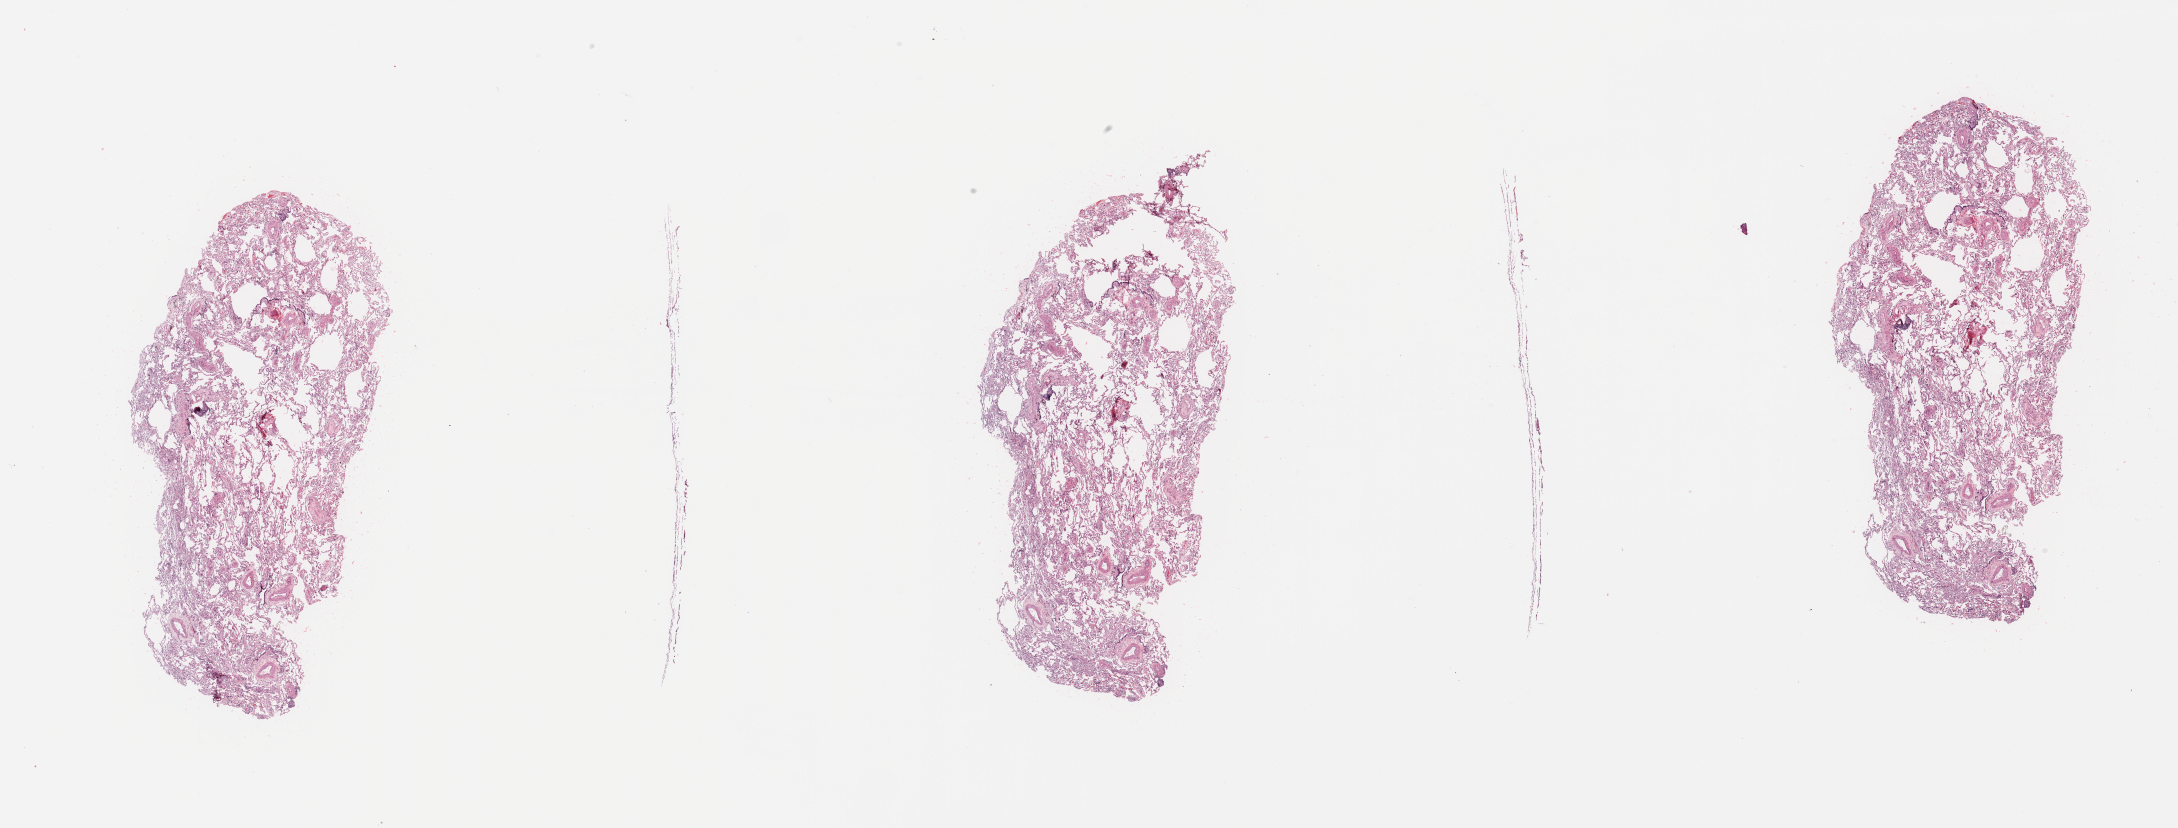
Hematoxylin and eosin (H&E) stained whole-slide image — low-resolution overview of the scanned area, about 34.5 x 13.1 mm, lung, tissue type not recorded.
• patient diagnosis (cohort enrolment): lung adenocarcinoma (lung)